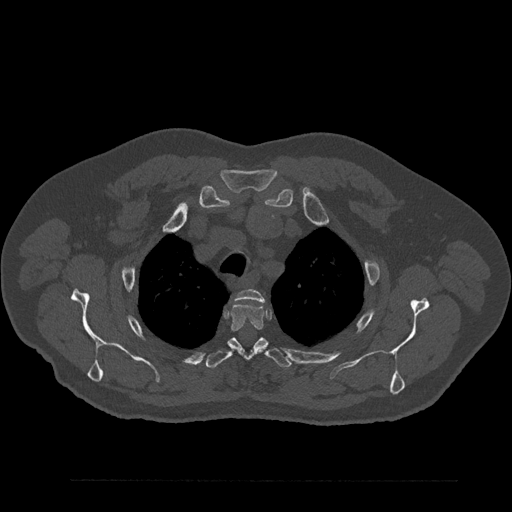
CT including the spine, one axial slice. Position 671 of 797 along the scan axis. Reconstruction kernel Br40s/3. 120 kVp. Bone window (W 1800 / L 400 HU). 512 × 512 image matrix, field of view 430 × 430 mm. Patient: male, 61 years. From the clinical record (not read from this slice): primary cancer: prostate.
Annotated regions visible in this slice (semi-automatic segmentation, software-assisted and operator-edited):
- T2 vertebra: box from (x=236, y=289) to (x=265, y=303) px
- T3 vertebra: (x=231, y=303)–(x=264, y=332)
- T4 vertebra: (x=206, y=337)–(x=291, y=369)